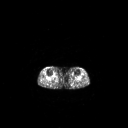
FDG PET of an extremity soft-tissue mass (from a PET/CT study), one axial slice. Position 159 of 267 along the scan axis. 3.27 mm slice thickness. 128 × 128 image matrix, field of view 700 × 700 mm. Female patient, age 65 years. Case-level facts recorded for this patient, not image findings: histological type: undifferentiated – high grade; grade: high; site of the primary tumour: right thigh.
Structures marked on this image (expert contour drawn on MRI and transferred to this co-registered scan by the dataset authors):
- gross tumour volume (mass): bounding box (x1, y1, x2, y2) in pixels: (54, 74, 56, 76)